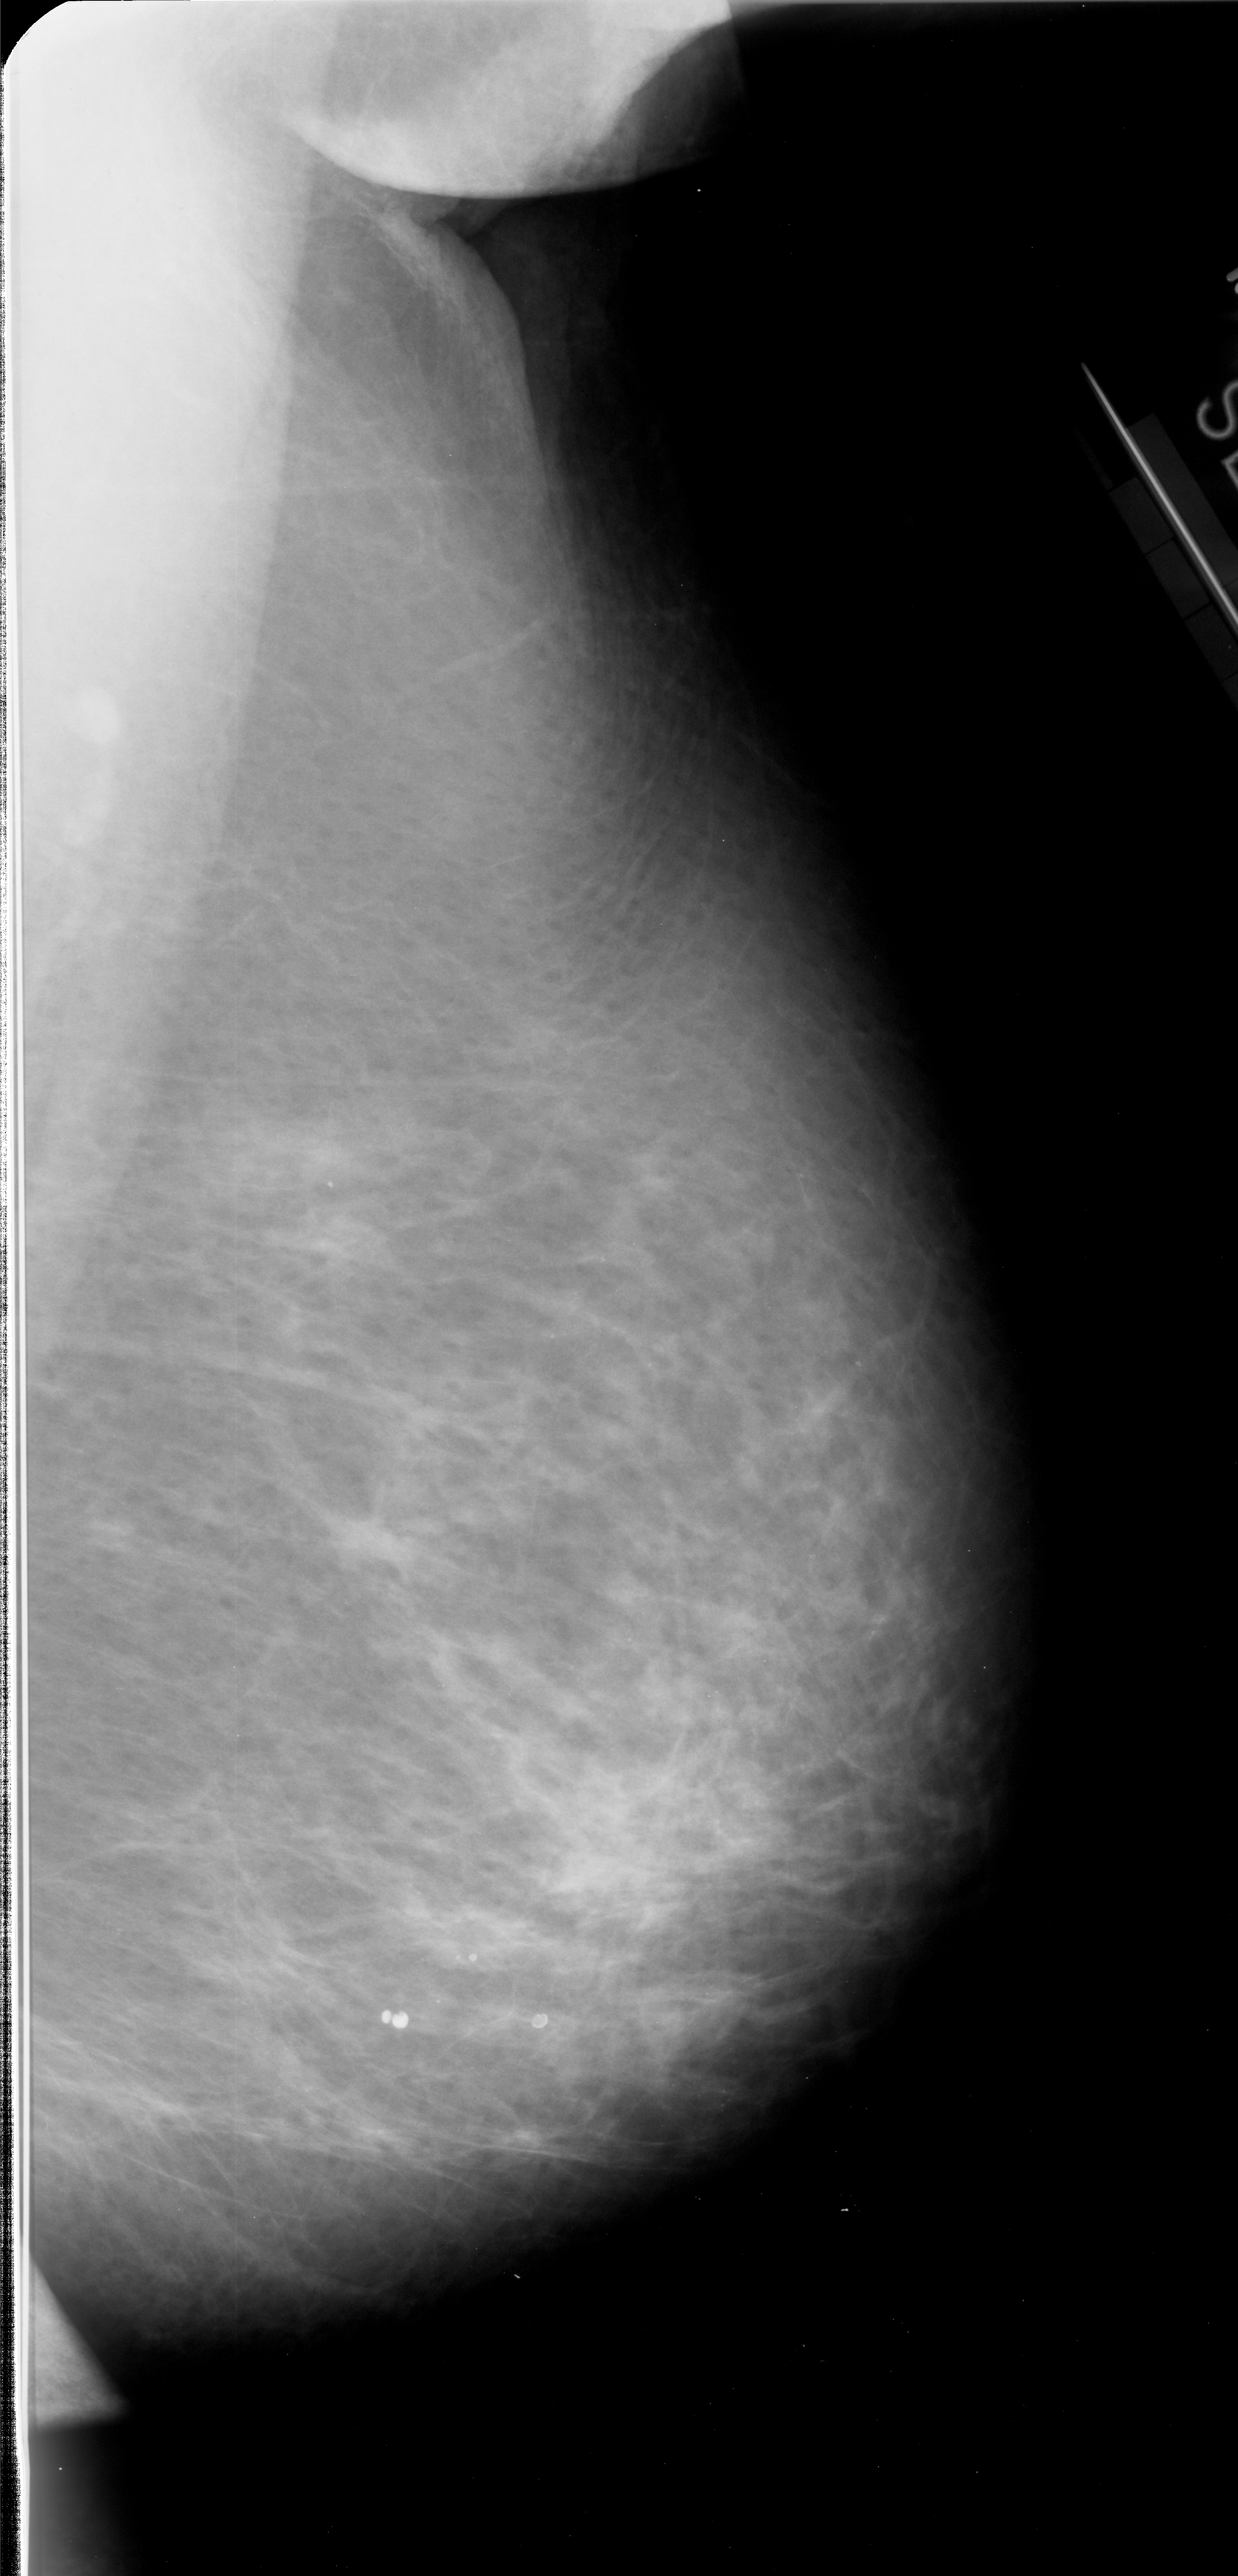
Digitized screen-film mammogram, right breast, mediolateral oblique (MLO) view, BI-RADS breast density category 2 (scale 1–4).
Marked abnormality: mass, shape irregular, margins spiculated; BI-RADS assessment category 4; pathology (as recorded): malignant.